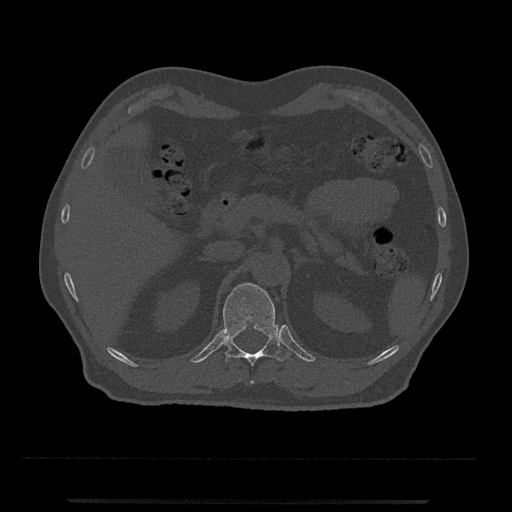
CT including the spine, one axial slice; slice 404 of 797 in the series (ordered by position); reconstruction kernel Br40s/3; 120 kVp; bone window (W 1800 / L 400 HU); 0.5 mm slice thickness; 512 × 512 image matrix. Patient: male, 63 years. From the clinical record (not read from this slice): primary cancer: prostate.
Structures marked on this image (semi-automatic segmentation, software-assisted and operator-edited):
- T12 vertebra: bounding box [x1, y1, x2, y2] px = [222, 283, 290, 384]